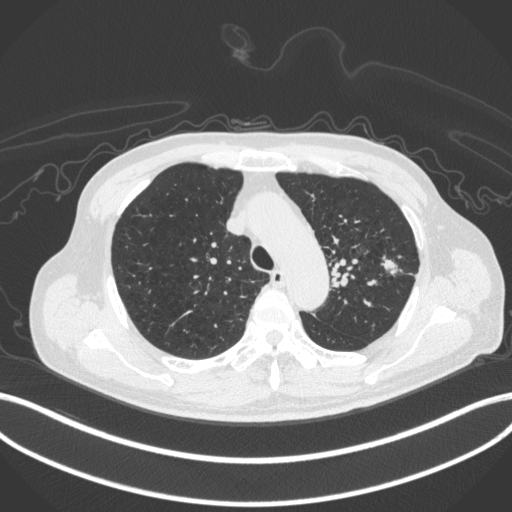
Chest CT, one axial slice; slice 331 of 420 in the series (ordered by position); reconstruction kernel B31f; lung window (W 1500 / L -600 HU); 1 mm slice thickness; 512 × 512 image matrix, field of view 400 × 400 mm. Male patient, age 77 years. From the clinical record (not read from this slice): clinical TNM (as recorded): T3 N1 M0.
Structures marked on this image (bounding box drawn by a radiologist):
- lung tumour (recorded histology: adenocarcinoma): bounding box [x1, y1, x2, y2] px = [380, 257, 402, 277]